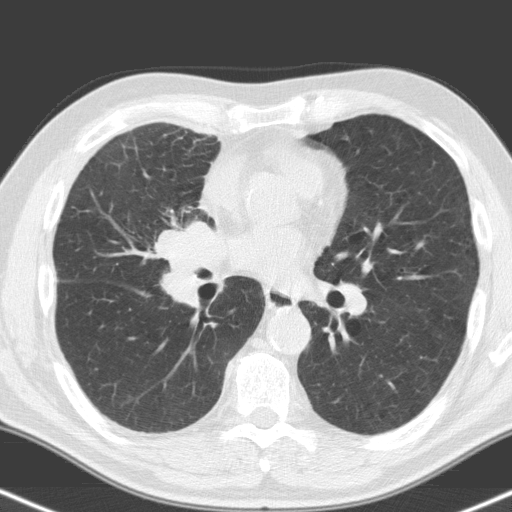
Low-dose screening chest CT, one axial slice. Slice 83 of 160 in the series (ordered by position). 120 kVp. Lung window (W 1500 / L -600 HU). 3.2 mm slice thickness. 512 × 512 image matrix, field of view 324 × 324 mm.
Annotated regions visible in this slice (outlined manually by an expert reader):
- lesion 1 (tumor, hilum of right lung): bounding box <158,222,225,306> (left, top, right, bottom; pixels)